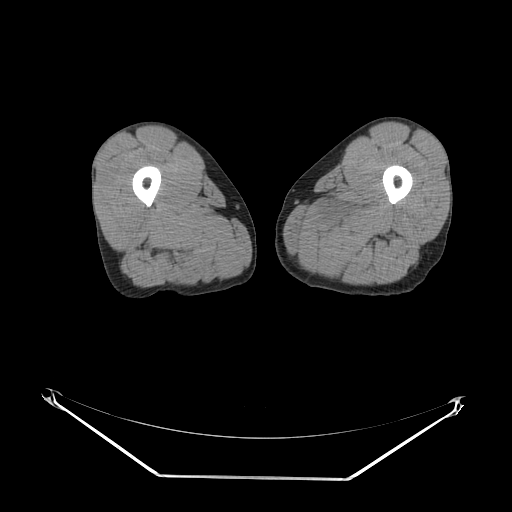
CT of an extremity soft-tissue mass (from a PET/CT study), one axial slice. Position 10 of 267 along the scan axis. 140 kVp. Soft-tissue window (W 400 / L 40 HU). 3.75 mm slice thickness. 512 × 512 image matrix, field of view 500 × 500 mm. Male patient. From the clinical record (not read from this slice): histological type: pleiomorphic liposarcoma; grade: high; site of the primary tumour: left thigh.
Annotated regions visible in this slice (expert contour drawn on MRI and transferred to this co-registered scan by the dataset authors):
- gross tumour volume including surrounding oedema: bounding box [x1, y1, x2, y2] px = [324, 201, 368, 232]